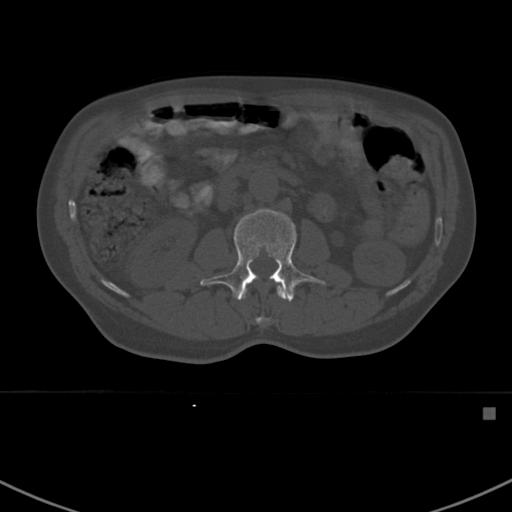
CT including the spine, one axial slice. Slice 289 of 412 in the series (ordered by position). Reconstruction kernel Br40s. Bone window (W 1800 / L 400 HU). 1.5 mm slice thickness. 512 × 512 image matrix, field of view 358 × 358 mm. Male patient, age 59 years. Case-level facts recorded for this patient, not image findings: primary cancer: prostate.
Structures marked on this image (semi-automatic segmentation, software-assisted and operator-edited):
- L1 vertebra: bounding box (x1, y1, x2, y2) in pixels: (244, 286, 286, 325)
- L2 vertebra: (200, 208, 326, 302)